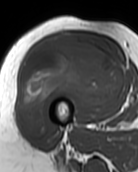
MRI of an extremity soft-tissue mass, one axial slice; slice 49 of 99 in the series (ordered by position); MR volume resampled by the dataset authors to the PET/CT grid (not the native acquisition matrix); 3.27 mm slice thickness; 138 × 172 image matrix, field of view 135 × 168 mm. Female patient. From the clinical record (not read from this slice): histological type: pleiomorphic undifferentiated sarcoma; grade: high; site of the primary tumour: right quadricep.
Annotated regions visible in this slice (expert contour drawn on MRI and transferred to this co-registered scan by the dataset authors):
- gross tumour volume including surrounding oedema: bounding box <19,34,123,136> (left, top, right, bottom; pixels)
- gross tumour volume (mass): <19,34,123,136>